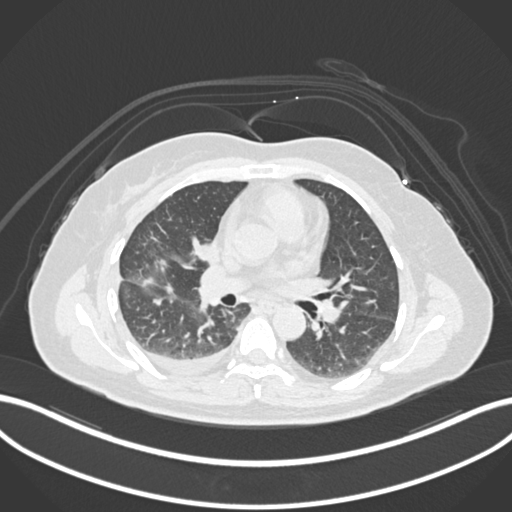
Chest CT, one axial slice; slice 73 of 172 in the series (ordered by position); reconstruction kernel B30f; 120 kVp; lung window (W 1500 / L -600 HU); 512 × 512 image matrix, field of view 400 × 400 mm. Female patient, age 52 years. Case-level facts recorded for this patient, not image findings: clinical TNM (as recorded): T3 N1 M1.
Outlined on this slice (bounding box drawn by a radiologist):
- lung tumour (recorded histology: adenocarcinoma): box from (x=191, y=236) to (x=217, y=262) px